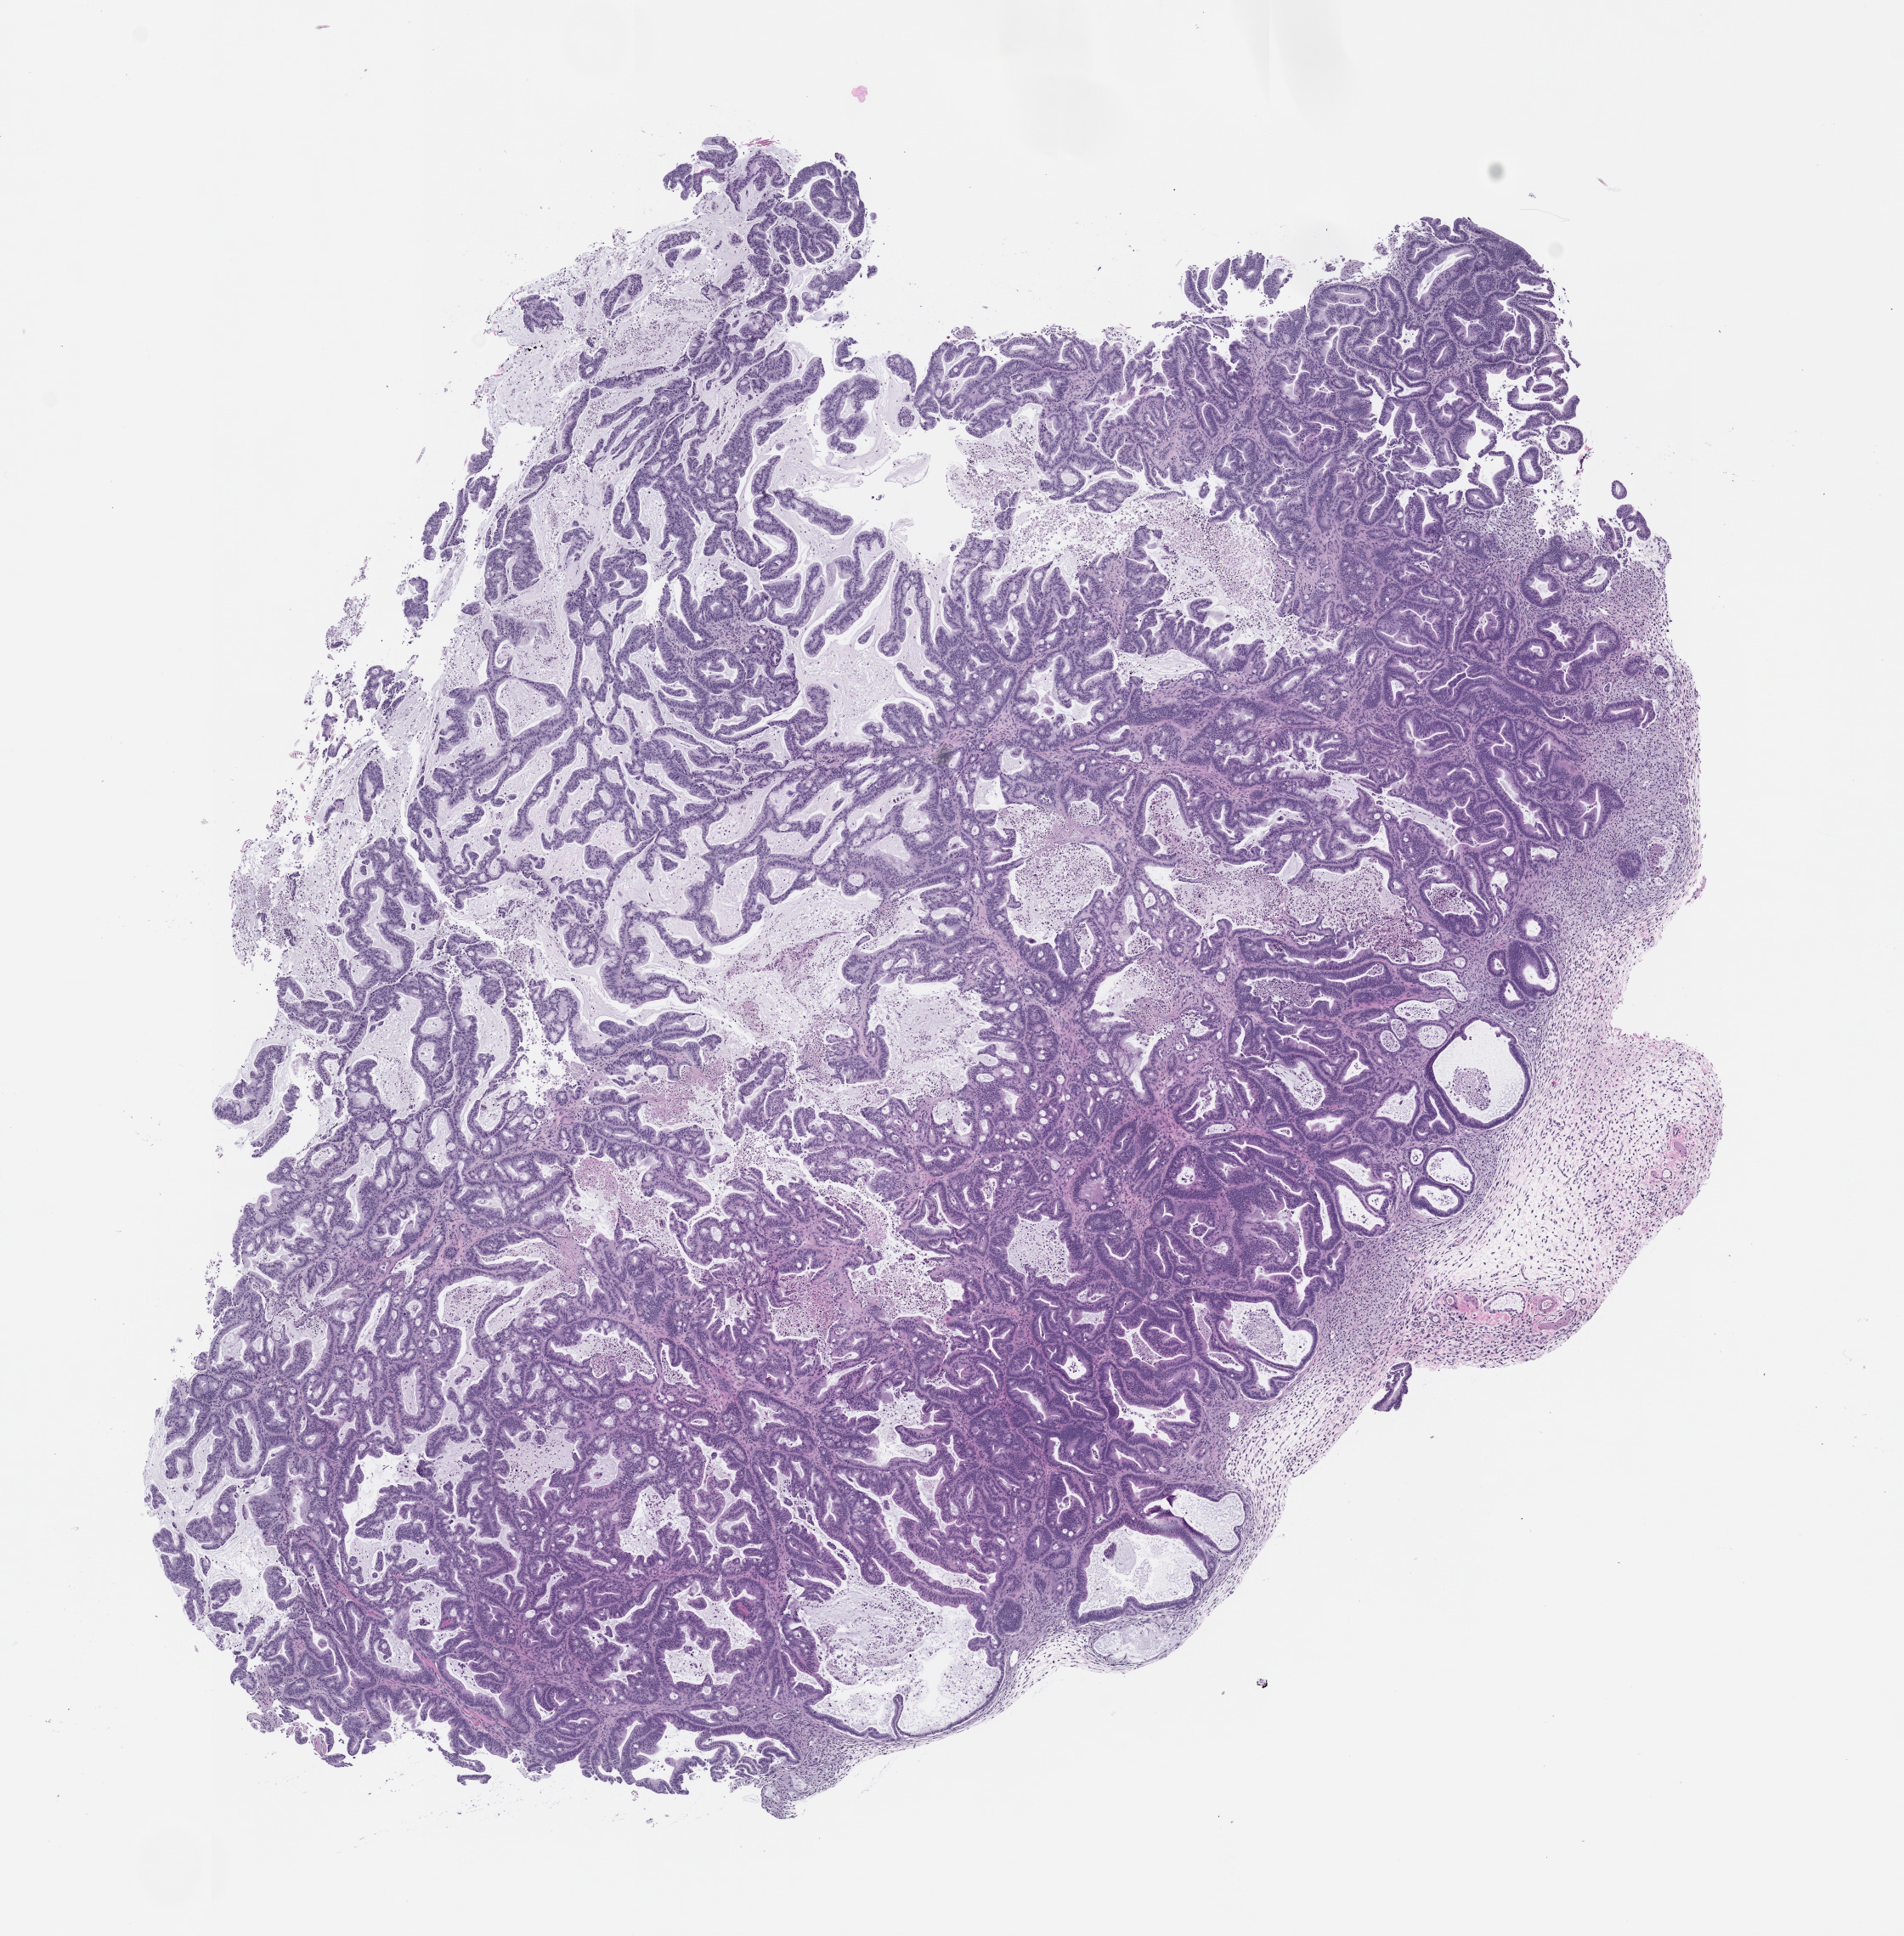
H&E whole-slide image of a patient-derived xenograft (PDX) tumor grown in a mouse, passage 2, a low-resolution overview of the entire scanned area, about 9.0 x 9.2 mm, FFPE section, tumor site category: pancreas.
Originating patient diagnosis: Pancreatic Adenocarcinoma.